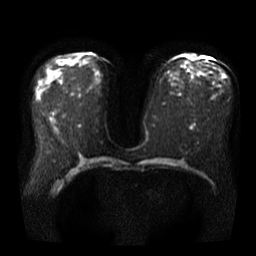
Breast MRI, one axial slice. Diffusion-weighted series; image 2 of 4 stored at this slice position (different b-values; order by instance number). 3 T. 5 mm slice thickness. 256 × 256 image matrix, field of view 360 × 360 mm. Female patient.
Outlined on this slice (manually delineated by an expert):
- tumour on diffusion-weighted imaging: bounding box [x1, y1, x2, y2] px = [189, 53, 196, 60]